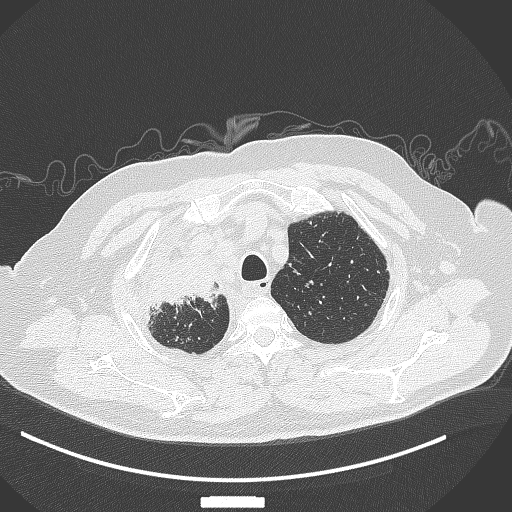
Chest CT, one axial slice; slice 310 of 384 in the series (ordered by position); reconstruction kernel B70f; lung window (W 1500 / L -600 HU); 1 mm slice thickness; 512 × 512 image matrix. Male patient, age 69 years. Case-level facts recorded for this patient, not image findings: clinical TNM (as recorded): T4 N3 M1.
Annotated regions visible in this slice (bounding box drawn by a radiologist):
- lung tumour (recorded histology: adenocarcinoma): bounding box [x1, y1, x2, y2] px = [142, 259, 226, 316]